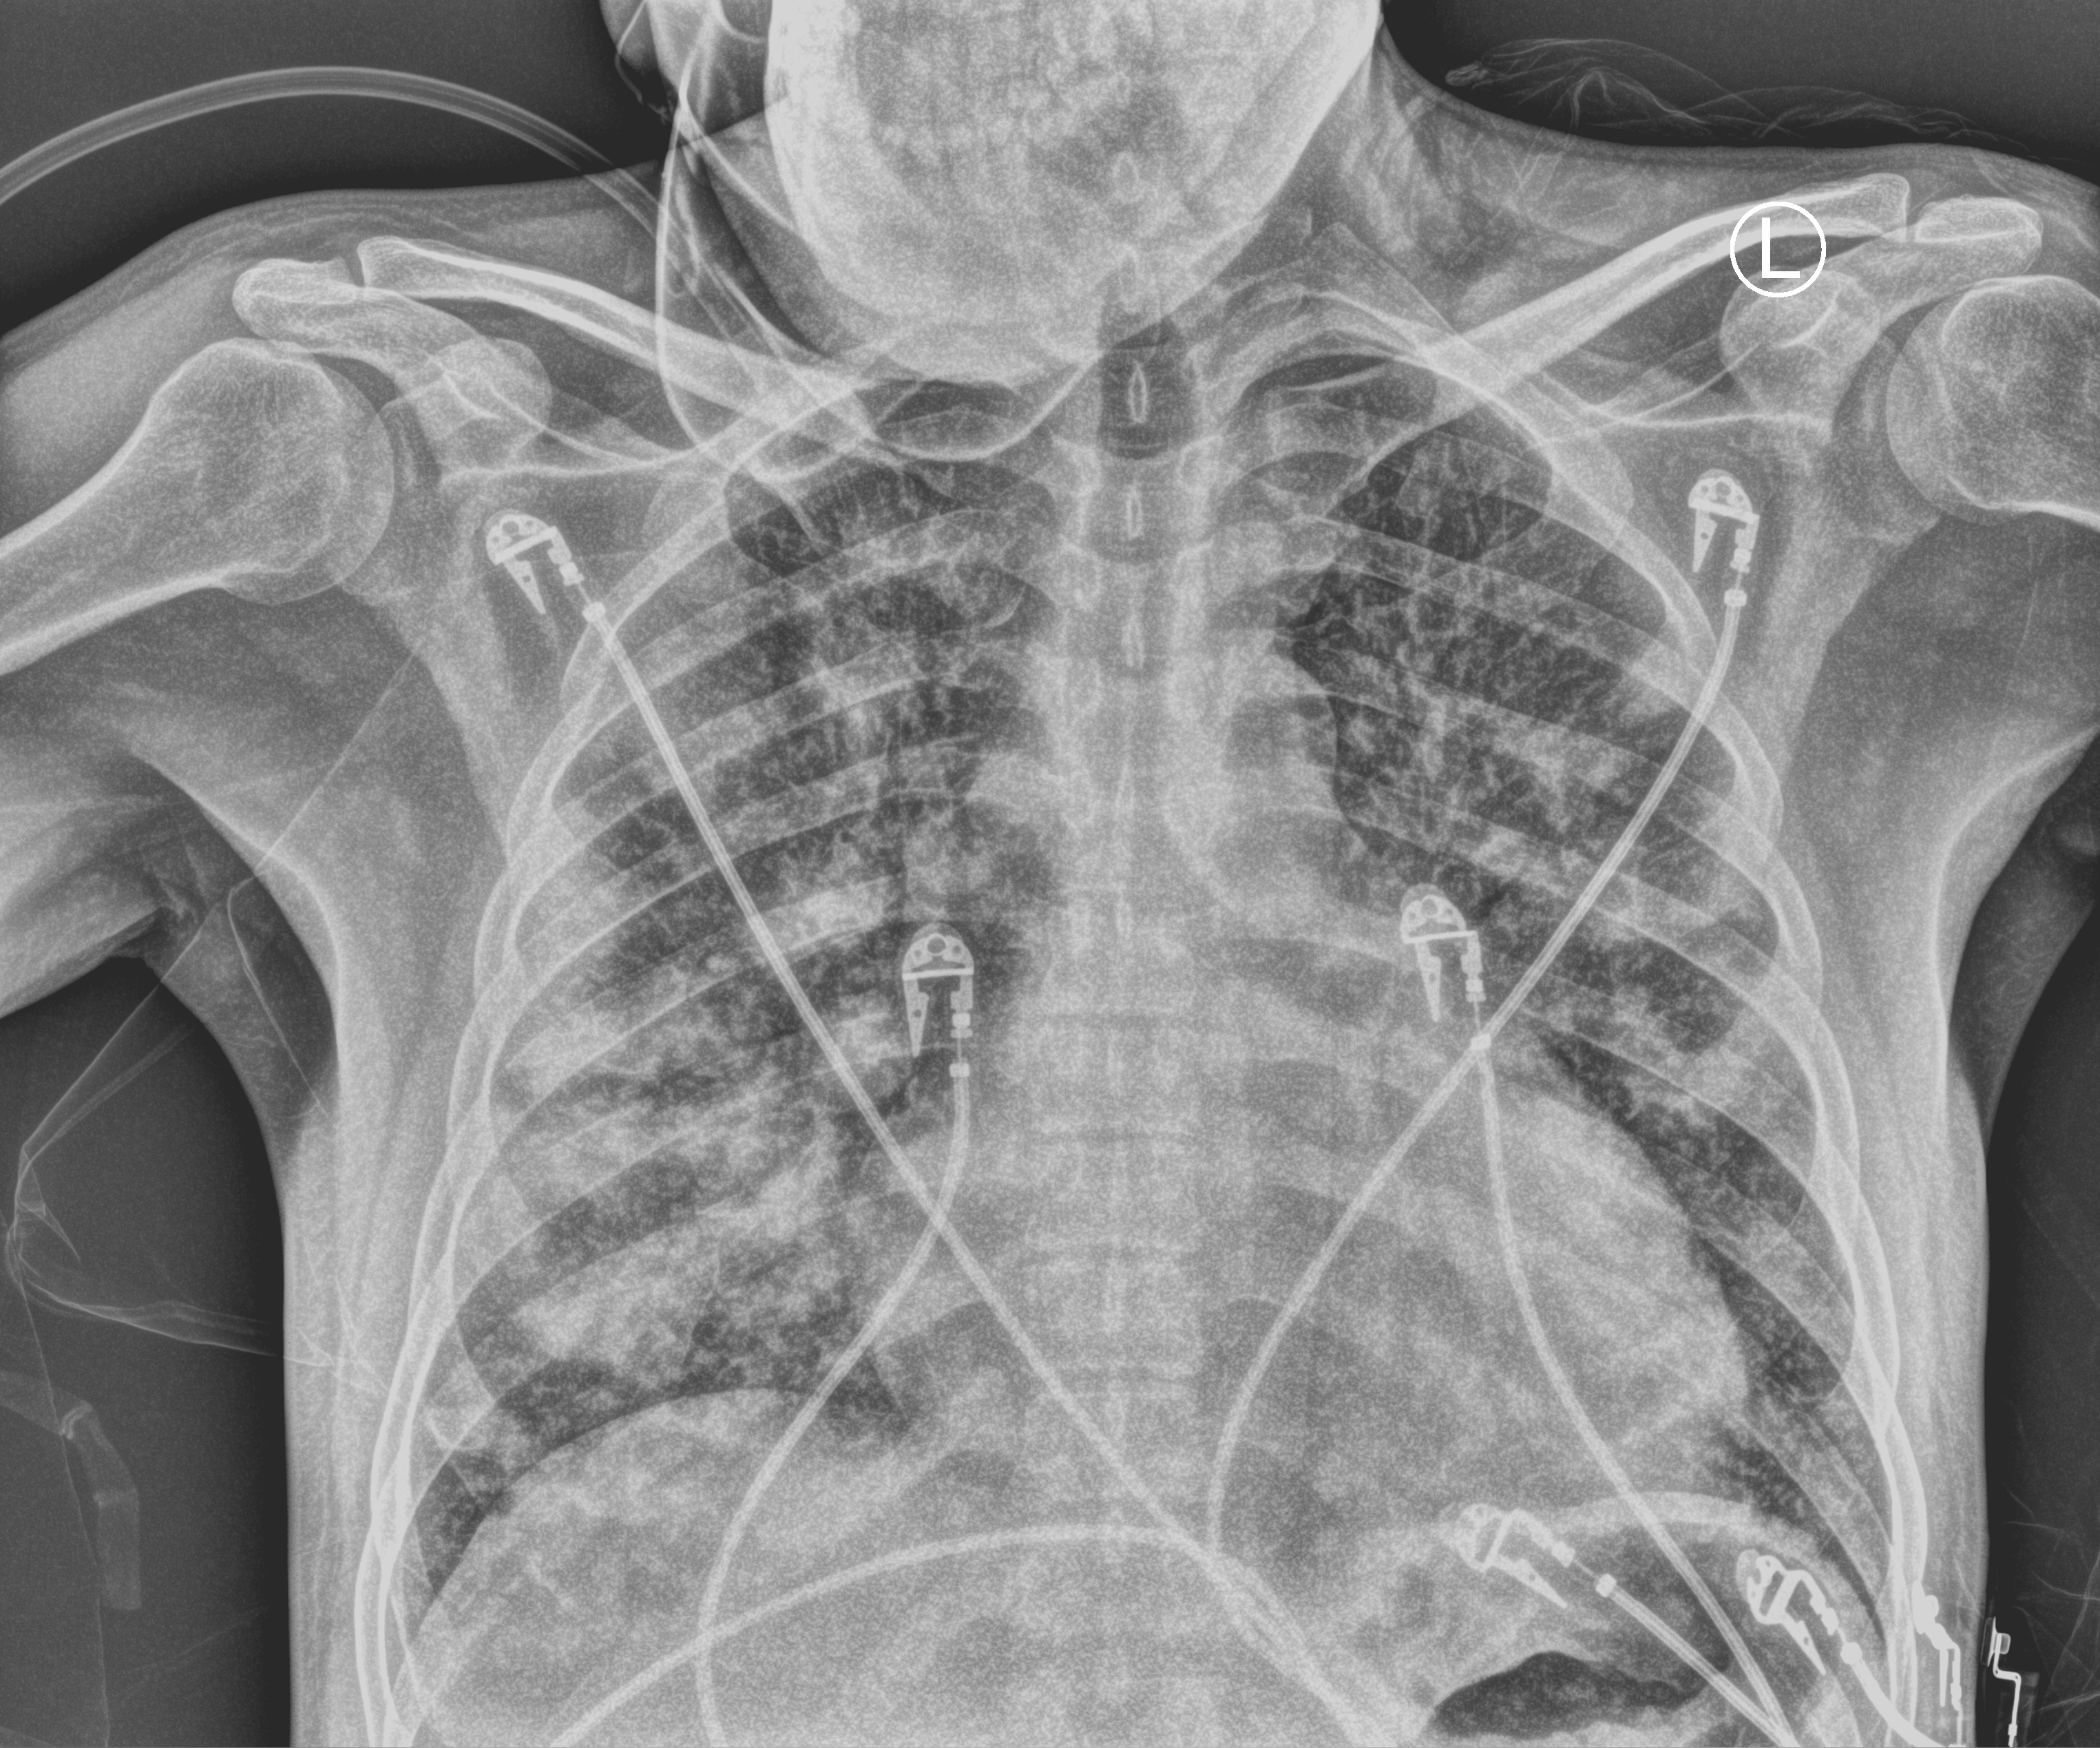
Portable chest radiograph; anteroposterior (AP) projection. Patient hospitalised with COVID-19; male, aged 18–59 years.
Admission-level facts for this patient (not findings on this image; timing relative to this image not recorded): COPD (admission record): no; other chronic lung disease (admission record): no.